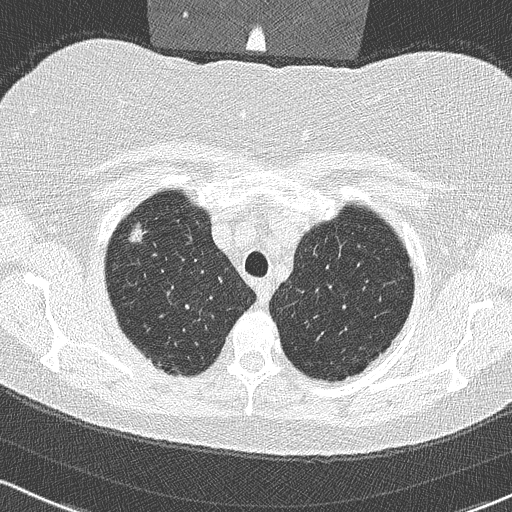
Chest CT (low-dose screening protocol), one axial image; third annual screen; lung window (W 1500 / L -600 HU); lung (sharp) reconstruction kernel (B50f); 120 kVp; slice 48 of 315 in the series. Female participant, aged 58 years at enrolment. Former smoker at enrolment.
Expert reader's lesion annotation, bounding box <120,218,160,254> (left, top, right, bottom; pixels). The screening reader recorded 2 non-calcified nodules or masses ≥4 mm on this exam; which of them this box marks is not recorded.